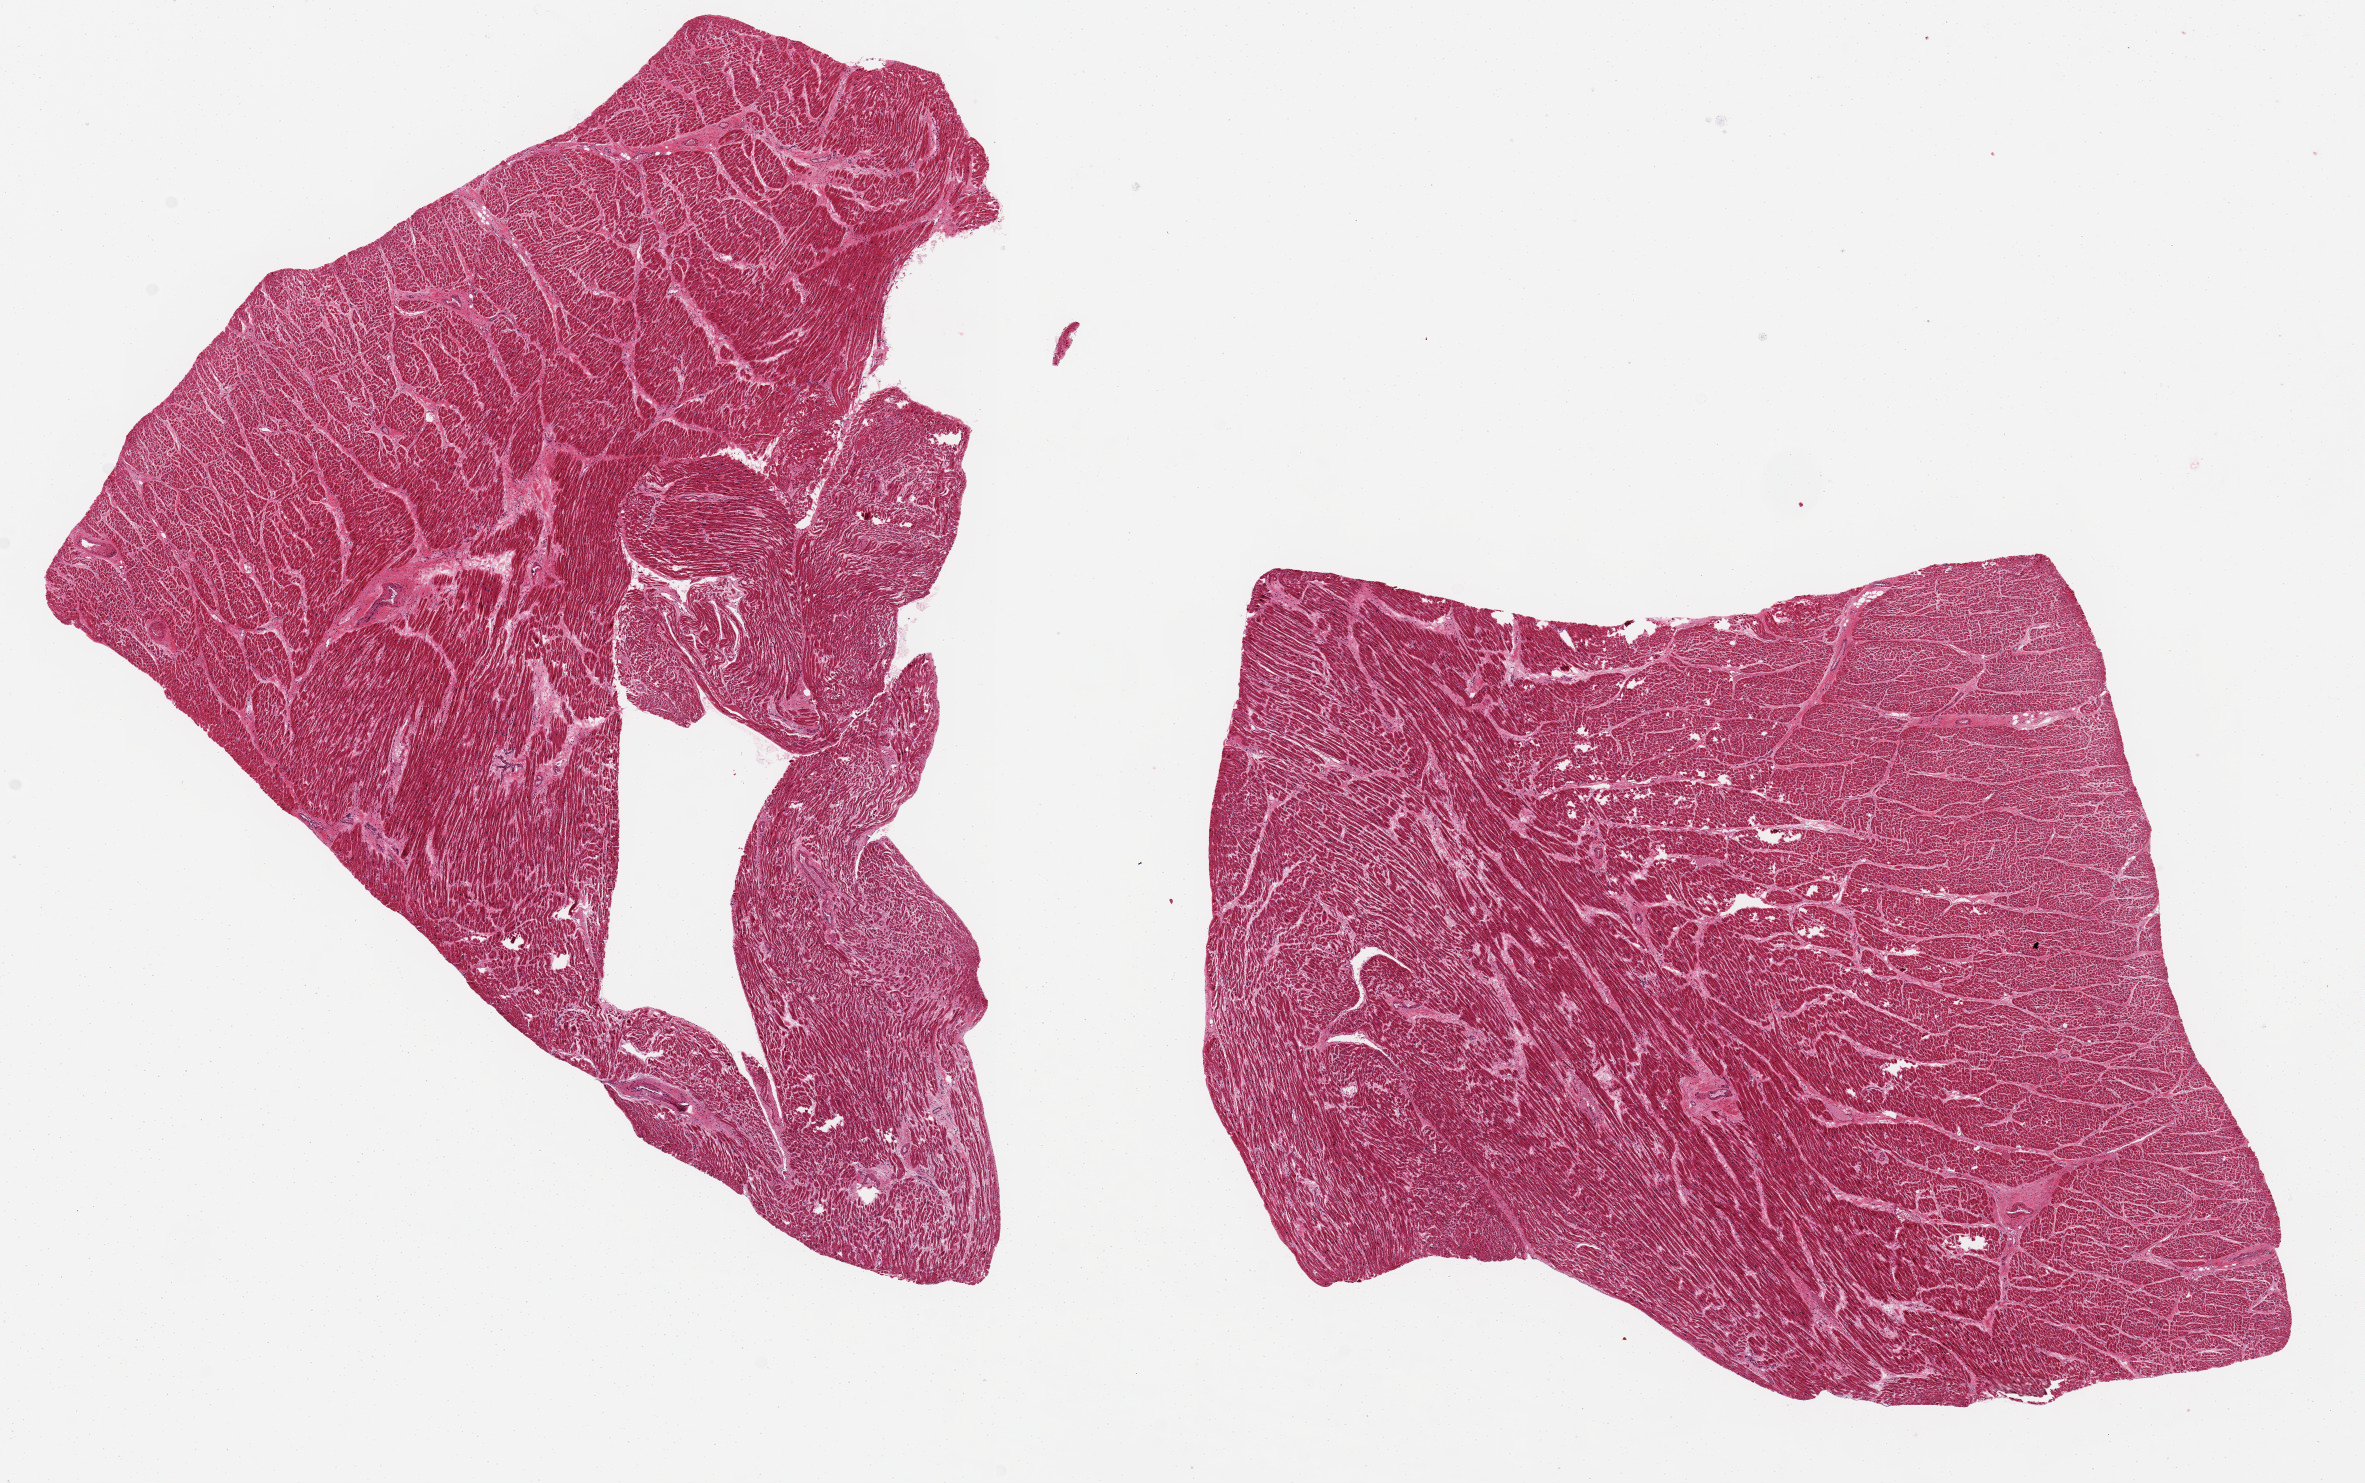
H&E whole-slide image — low-resolution overview of the scanned area, about 18.7 x 11.7 mm, PAXgene-fixed, paraffin-embedded tissue, section of heart (target tissue), donor tissue sample. Donor: female.
Pathologist's review note for this sample: 2 ~8x6.5mm aliquots , patchy interstitial fibrosis in each.